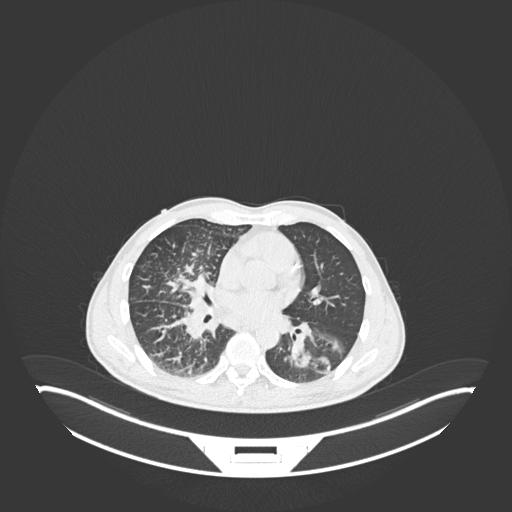
Chest CT, one axial slice; slice 116 of 237 in the series (ordered by position); reconstruction kernel B30f; 120 kVp; lung window (W 1500 / L -600 HU); 1 mm slice thickness; 512 × 512 image matrix. Patient: male, 49 years. Case-level facts recorded for this patient, not image findings: clinical TNM (as recorded): T2b N1 M0.
Annotated regions visible in this slice (bounding box drawn by a radiologist):
- lung tumour (recorded histology: adenocarcinoma): bounding box [x1, y1, x2, y2] px = [290, 319, 350, 378]